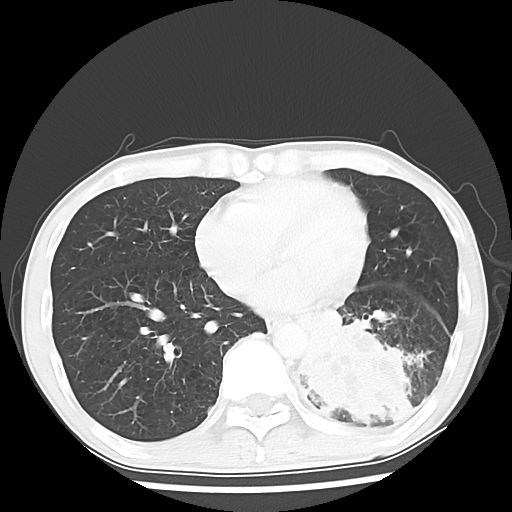
Chest CT, one axial slice. Lung window (W 1500 / L -600 HU). 512 × 512 image matrix, field of view 313 × 313 mm. Patient: male, 68 years. From the clinical record (not read from this slice): clinical TNM (as recorded): T4 N0 M0.
Structures marked on this image (rectangle marked by the reading radiologist):
- lung tumour (recorded histology: squamous cell carcinoma): box from (x=289, y=314) to (x=421, y=437) px